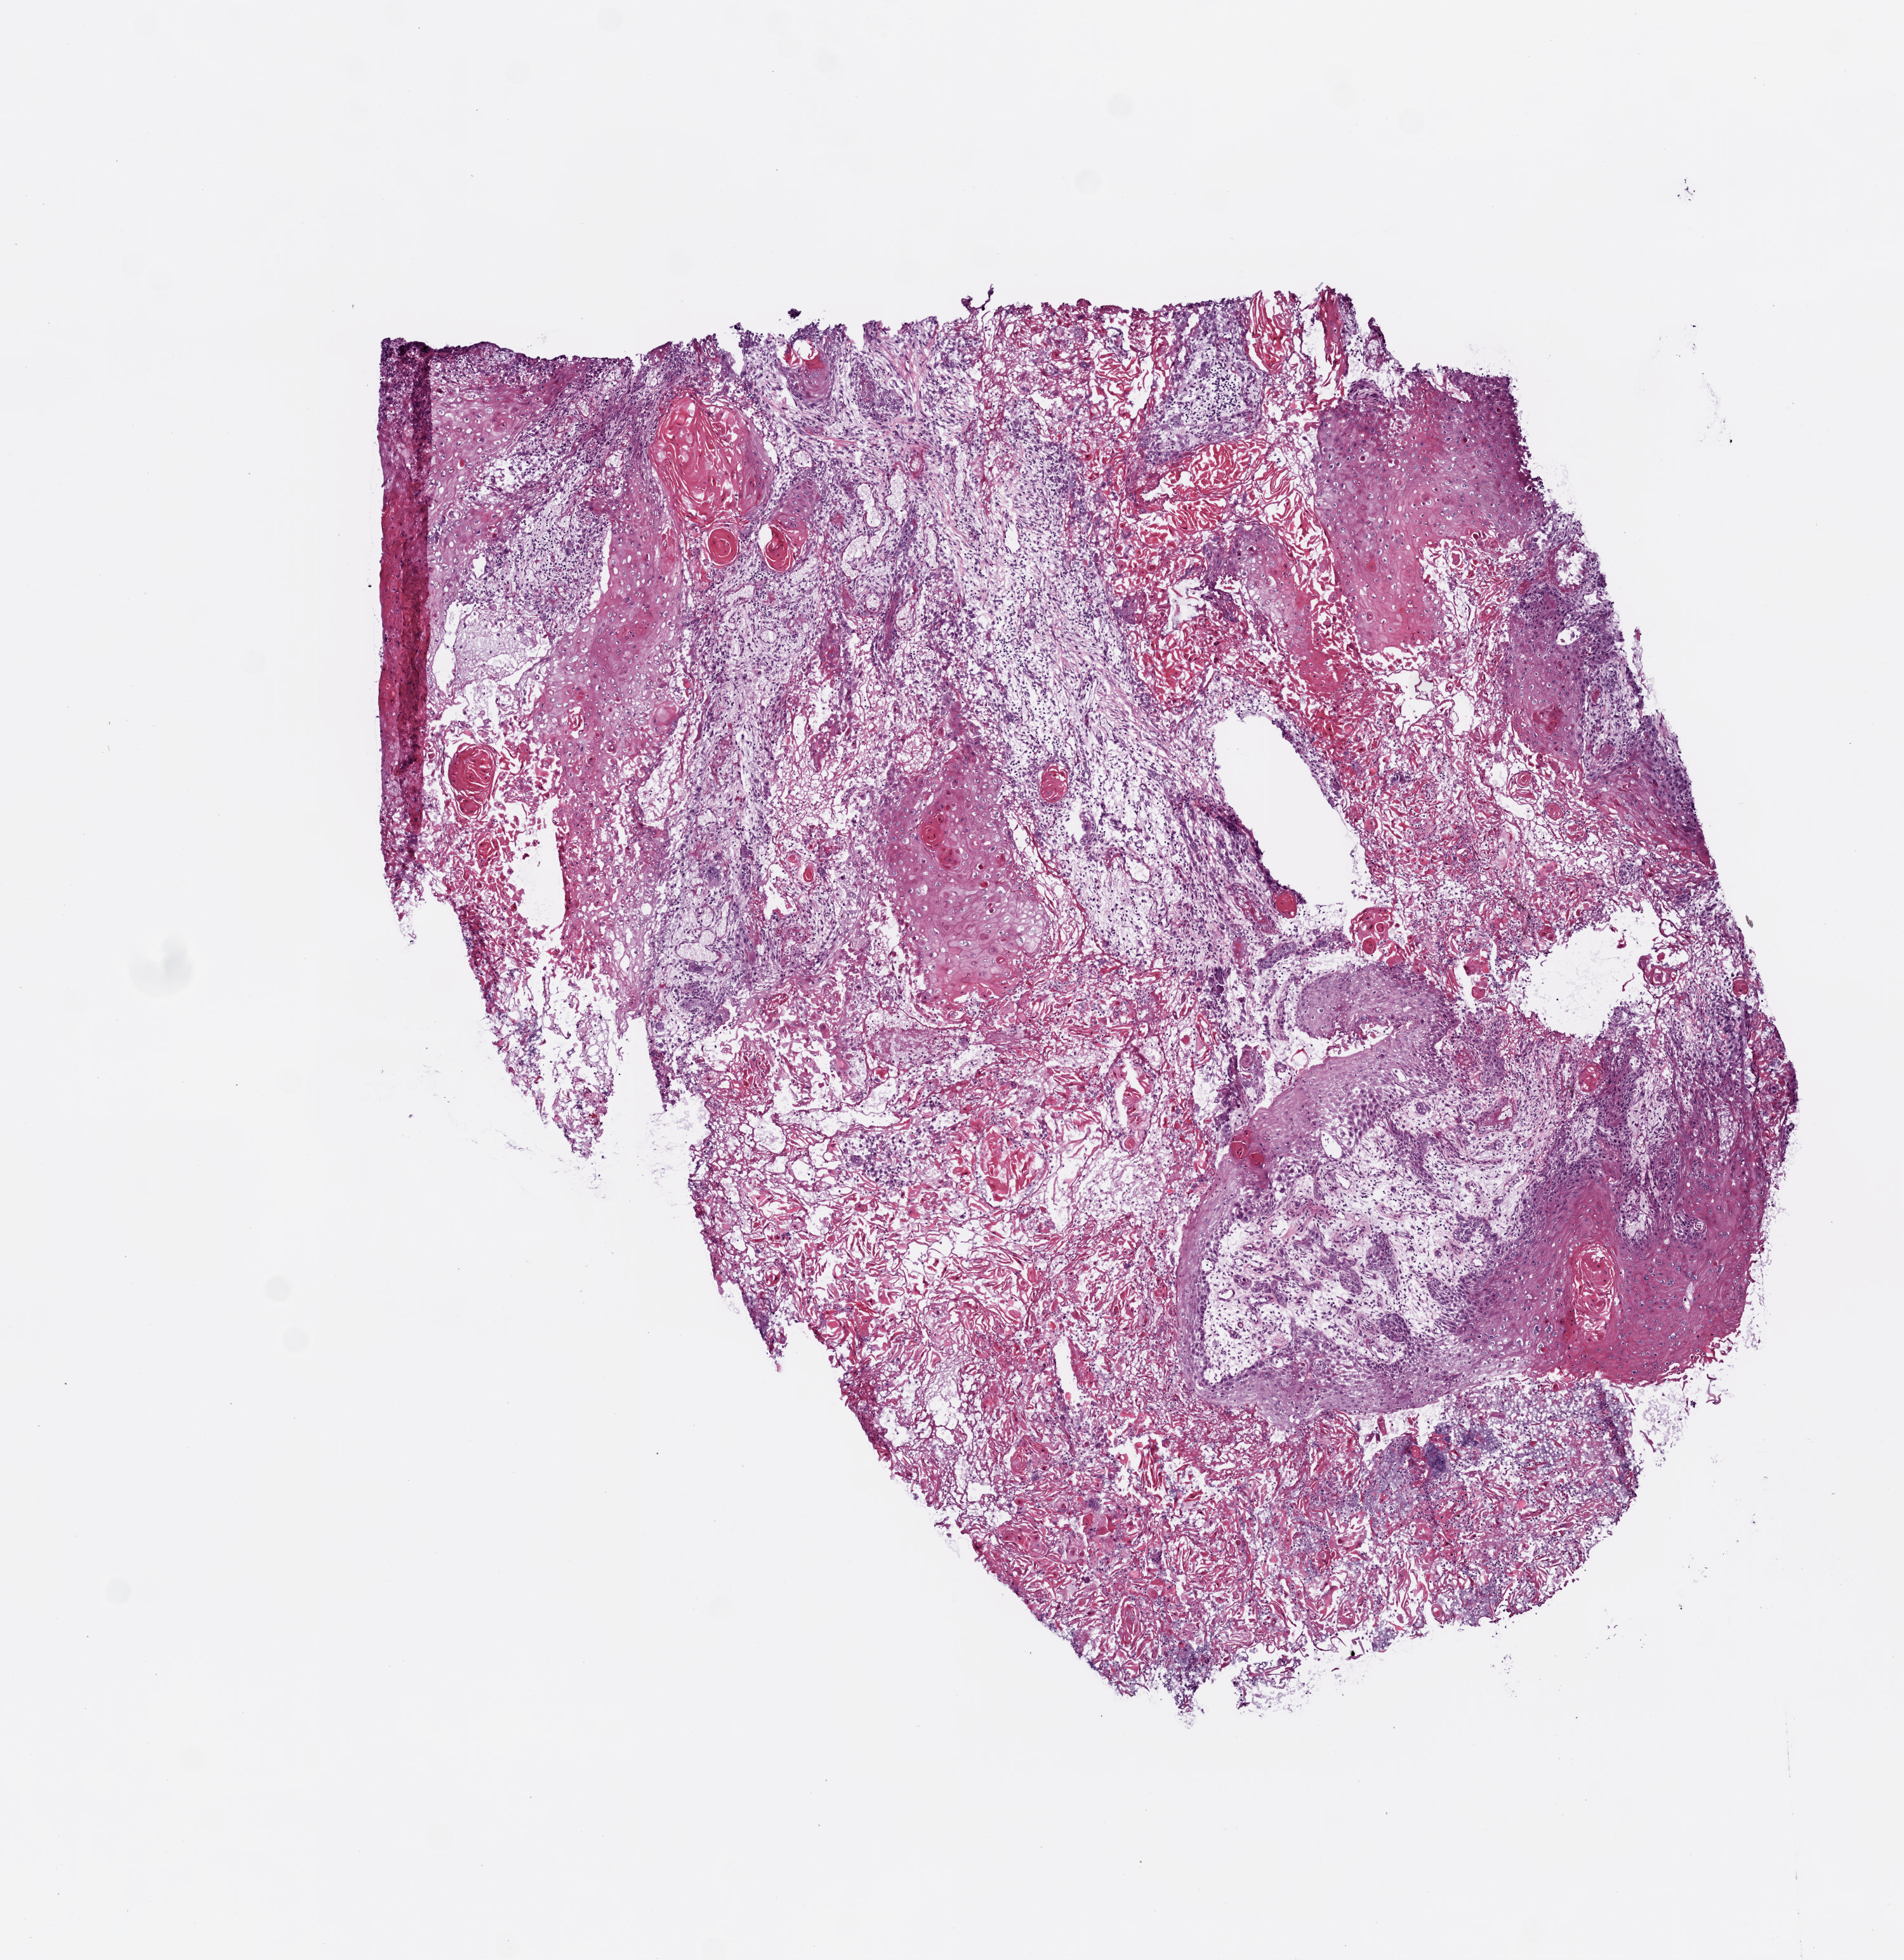
Digitized Hematoxylin and eosin (H&E) stained tissue section (whole slide), a low-resolution overview of the entire scanned area, about 6.0 x 6.2 mm; frozen section from the top of the tissue portion; sample: primary tumour, head and neck. Patient: female, age at initial diagnosis 41 years. Histologic grade: G2 (moderately differentiated). Pathologist review of this section (percent, as recorded): tumour cells 80%, tumour nuclei 75%, normal cells 0%, stromal cells 20%, necrosis 0%.
Laterality: right. Lymph nodes positive (case pathology): 1 of 34 examined. Pathologic diagnosis: Squamous cell carcinoma, NOS. AJCC pathologic stage: III (7th edition).